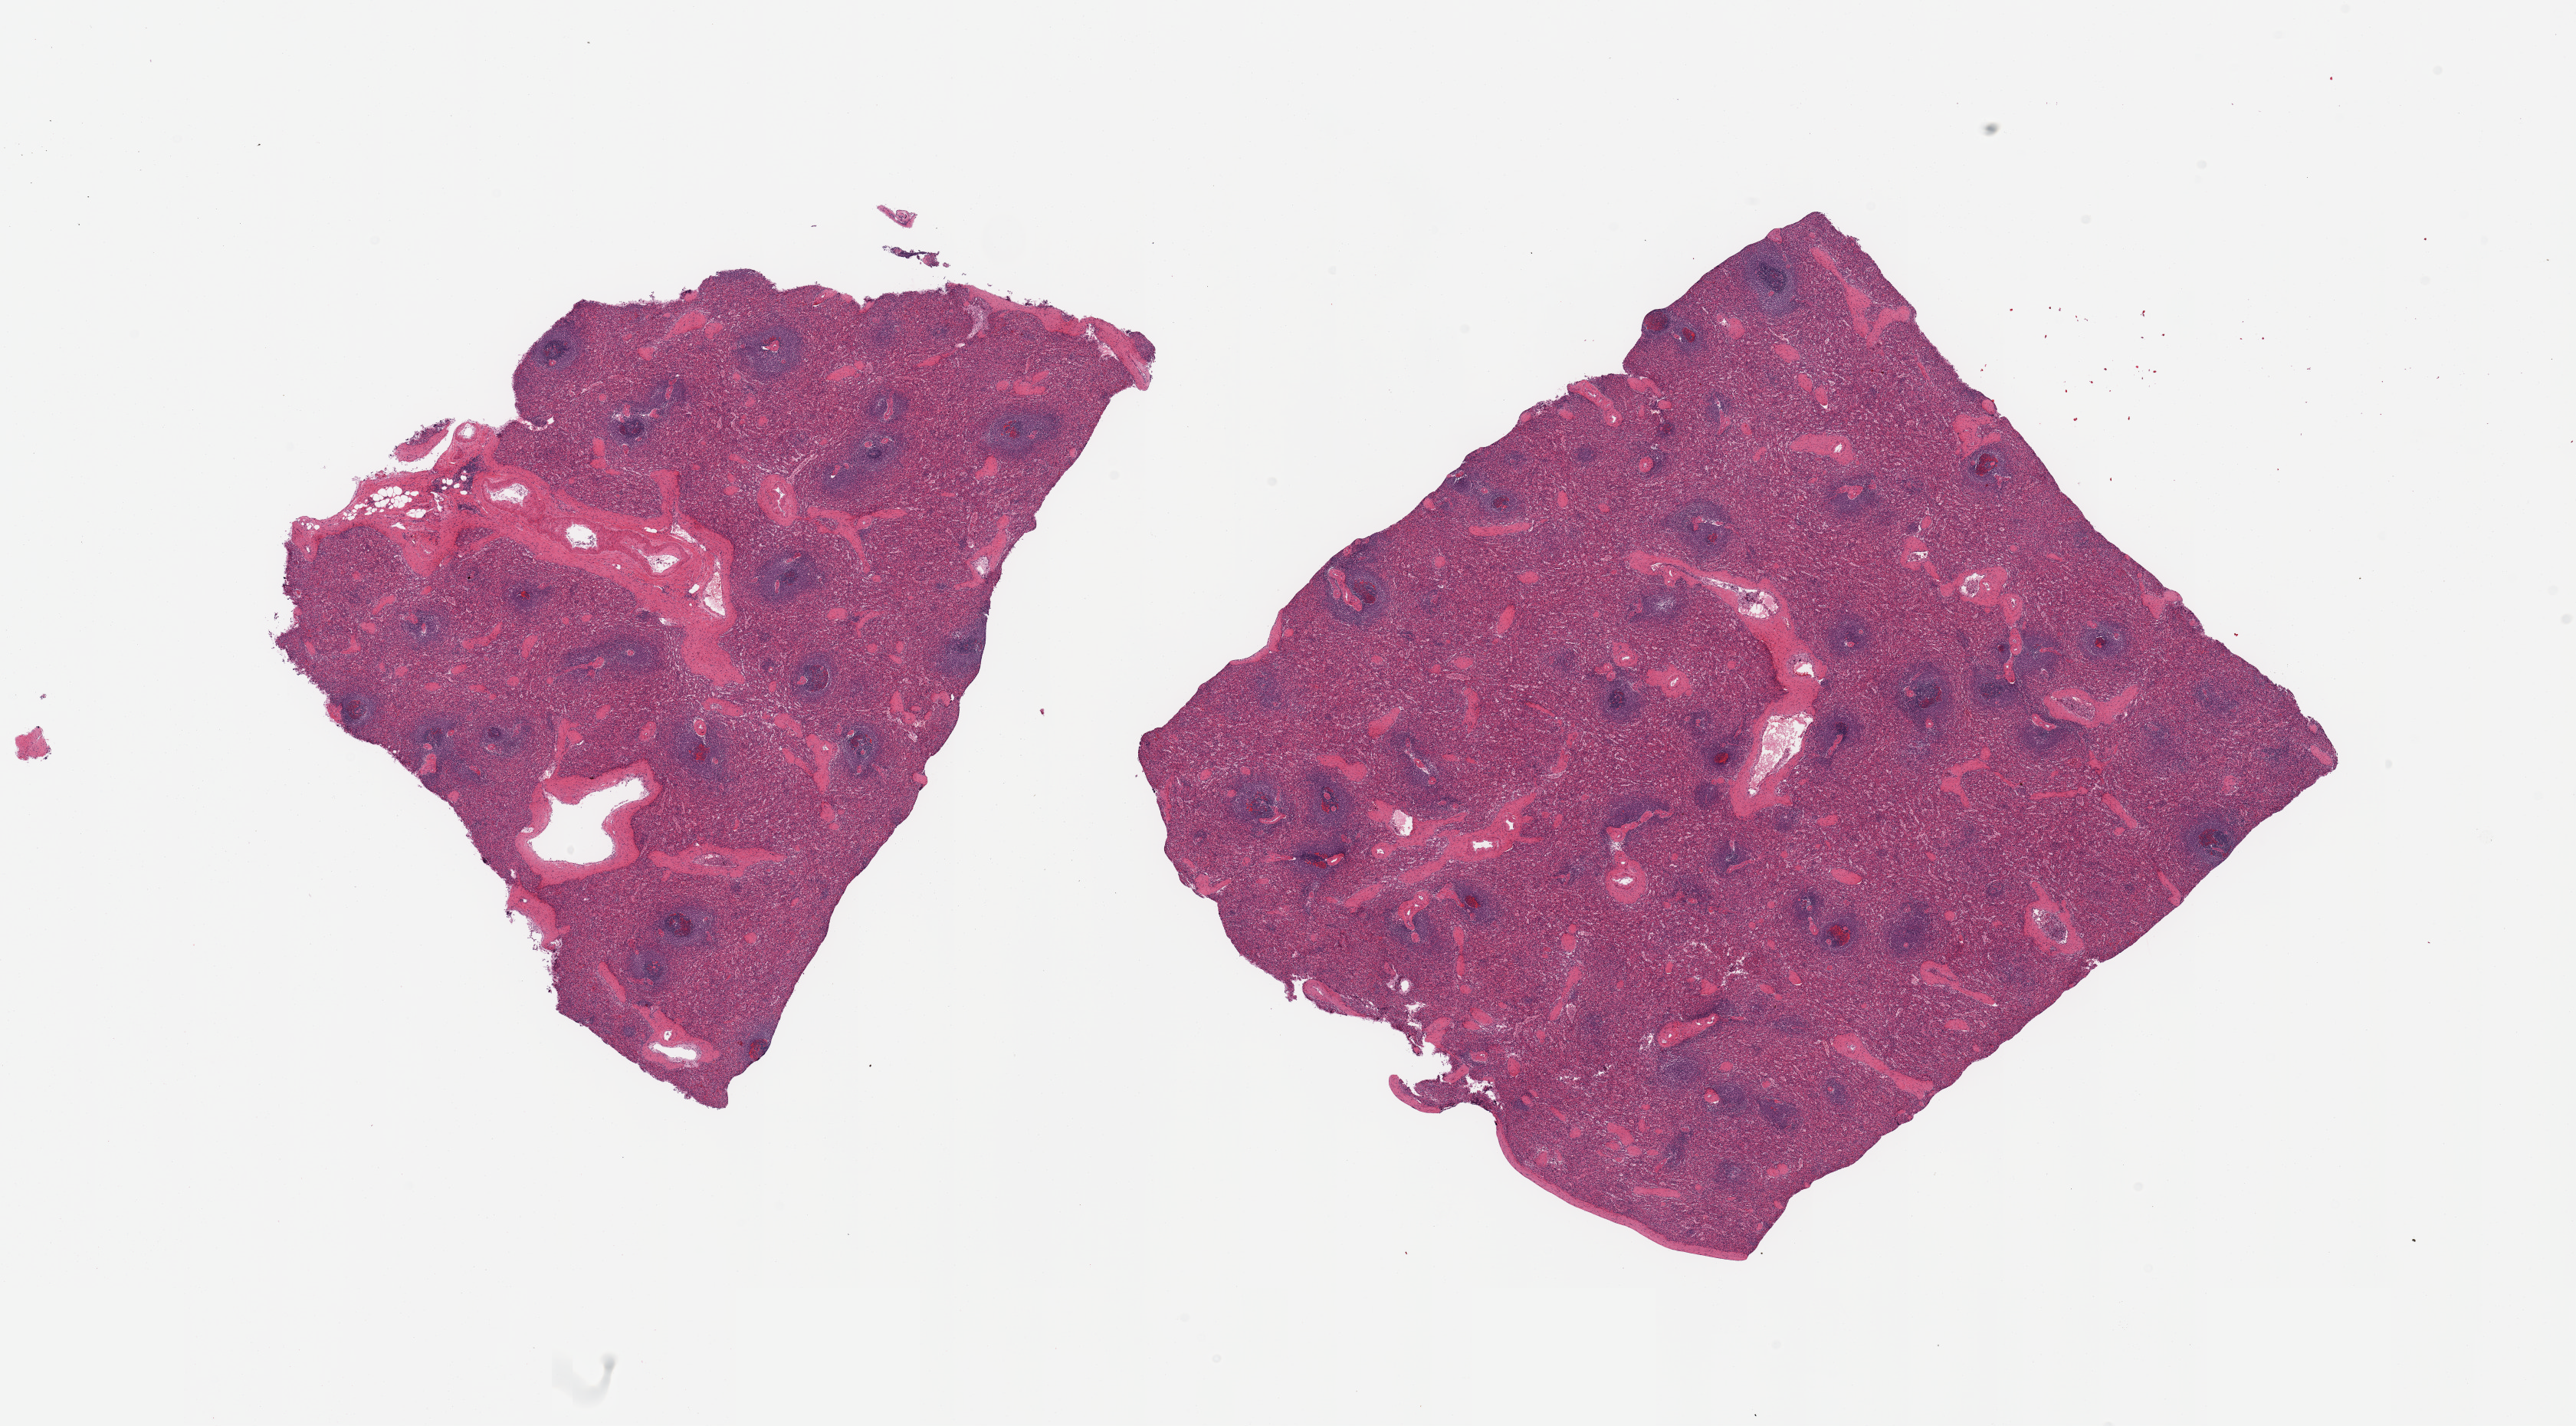
Whole-slide image, H&E stain — shown as a low-resolution overview of the whole scanned area (about 26.6 x 14.7 mm, acquisition: 20x scan). PAXgene-fixed, paraffin-embedded tissue. Sampled site (target tissue): spleen. Tissue donor sample.
* reviewer comment on this tissue sample: 2 pieces; no congestion